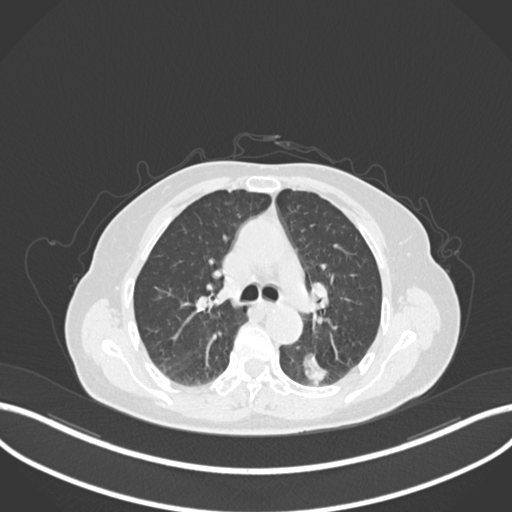
Chest CT, one axial slice; 120 kVp; lung window (W 1500 / L -600 HU); 512 × 512 image matrix, field of view 400 × 400 mm. Patient: female, 70 years. Case-level facts recorded for this patient, not image findings: clinical TNM (as recorded): T1c N0 M0.
Outlined on this slice (bounding box drawn by a radiologist):
- lung tumour (recorded histology: adenocarcinoma): bounding box (x1, y1, x2, y2) in pixels: (302, 347, 332, 385)